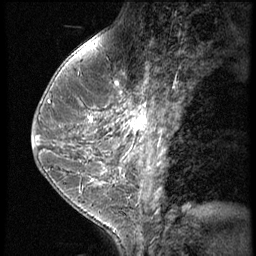
Breast MRI (dynamic contrast-enhanced), one sagittal slice; slice 24 of 60 in the series (ordered by position); 3 images stored at this slice position (order not interpretable as contrast timing); 1.5 T; TE 4.2 ms, TR 9 ms; 256 × 256 image matrix, field of view 180 × 180 mm. Patient: female, 38 years. Case-level facts recorded for this patient, not image findings: setting: breast cancer imaged before/during neoadjuvant chemotherapy; receptor status: triple-negative.
Annotated regions visible in this slice (semi-automatically segmented with operator editing):
- analysis volume of interest (the breast-tissue region the enhancement analysis was run in; not a lesion): bounding box [x1, y1, x2, y2] px = [119, 93, 165, 150]
- tumour enhancement mask (voxels above the 140 % enhancement threshold inside the analysis volume of interest): [122, 103, 147, 133]